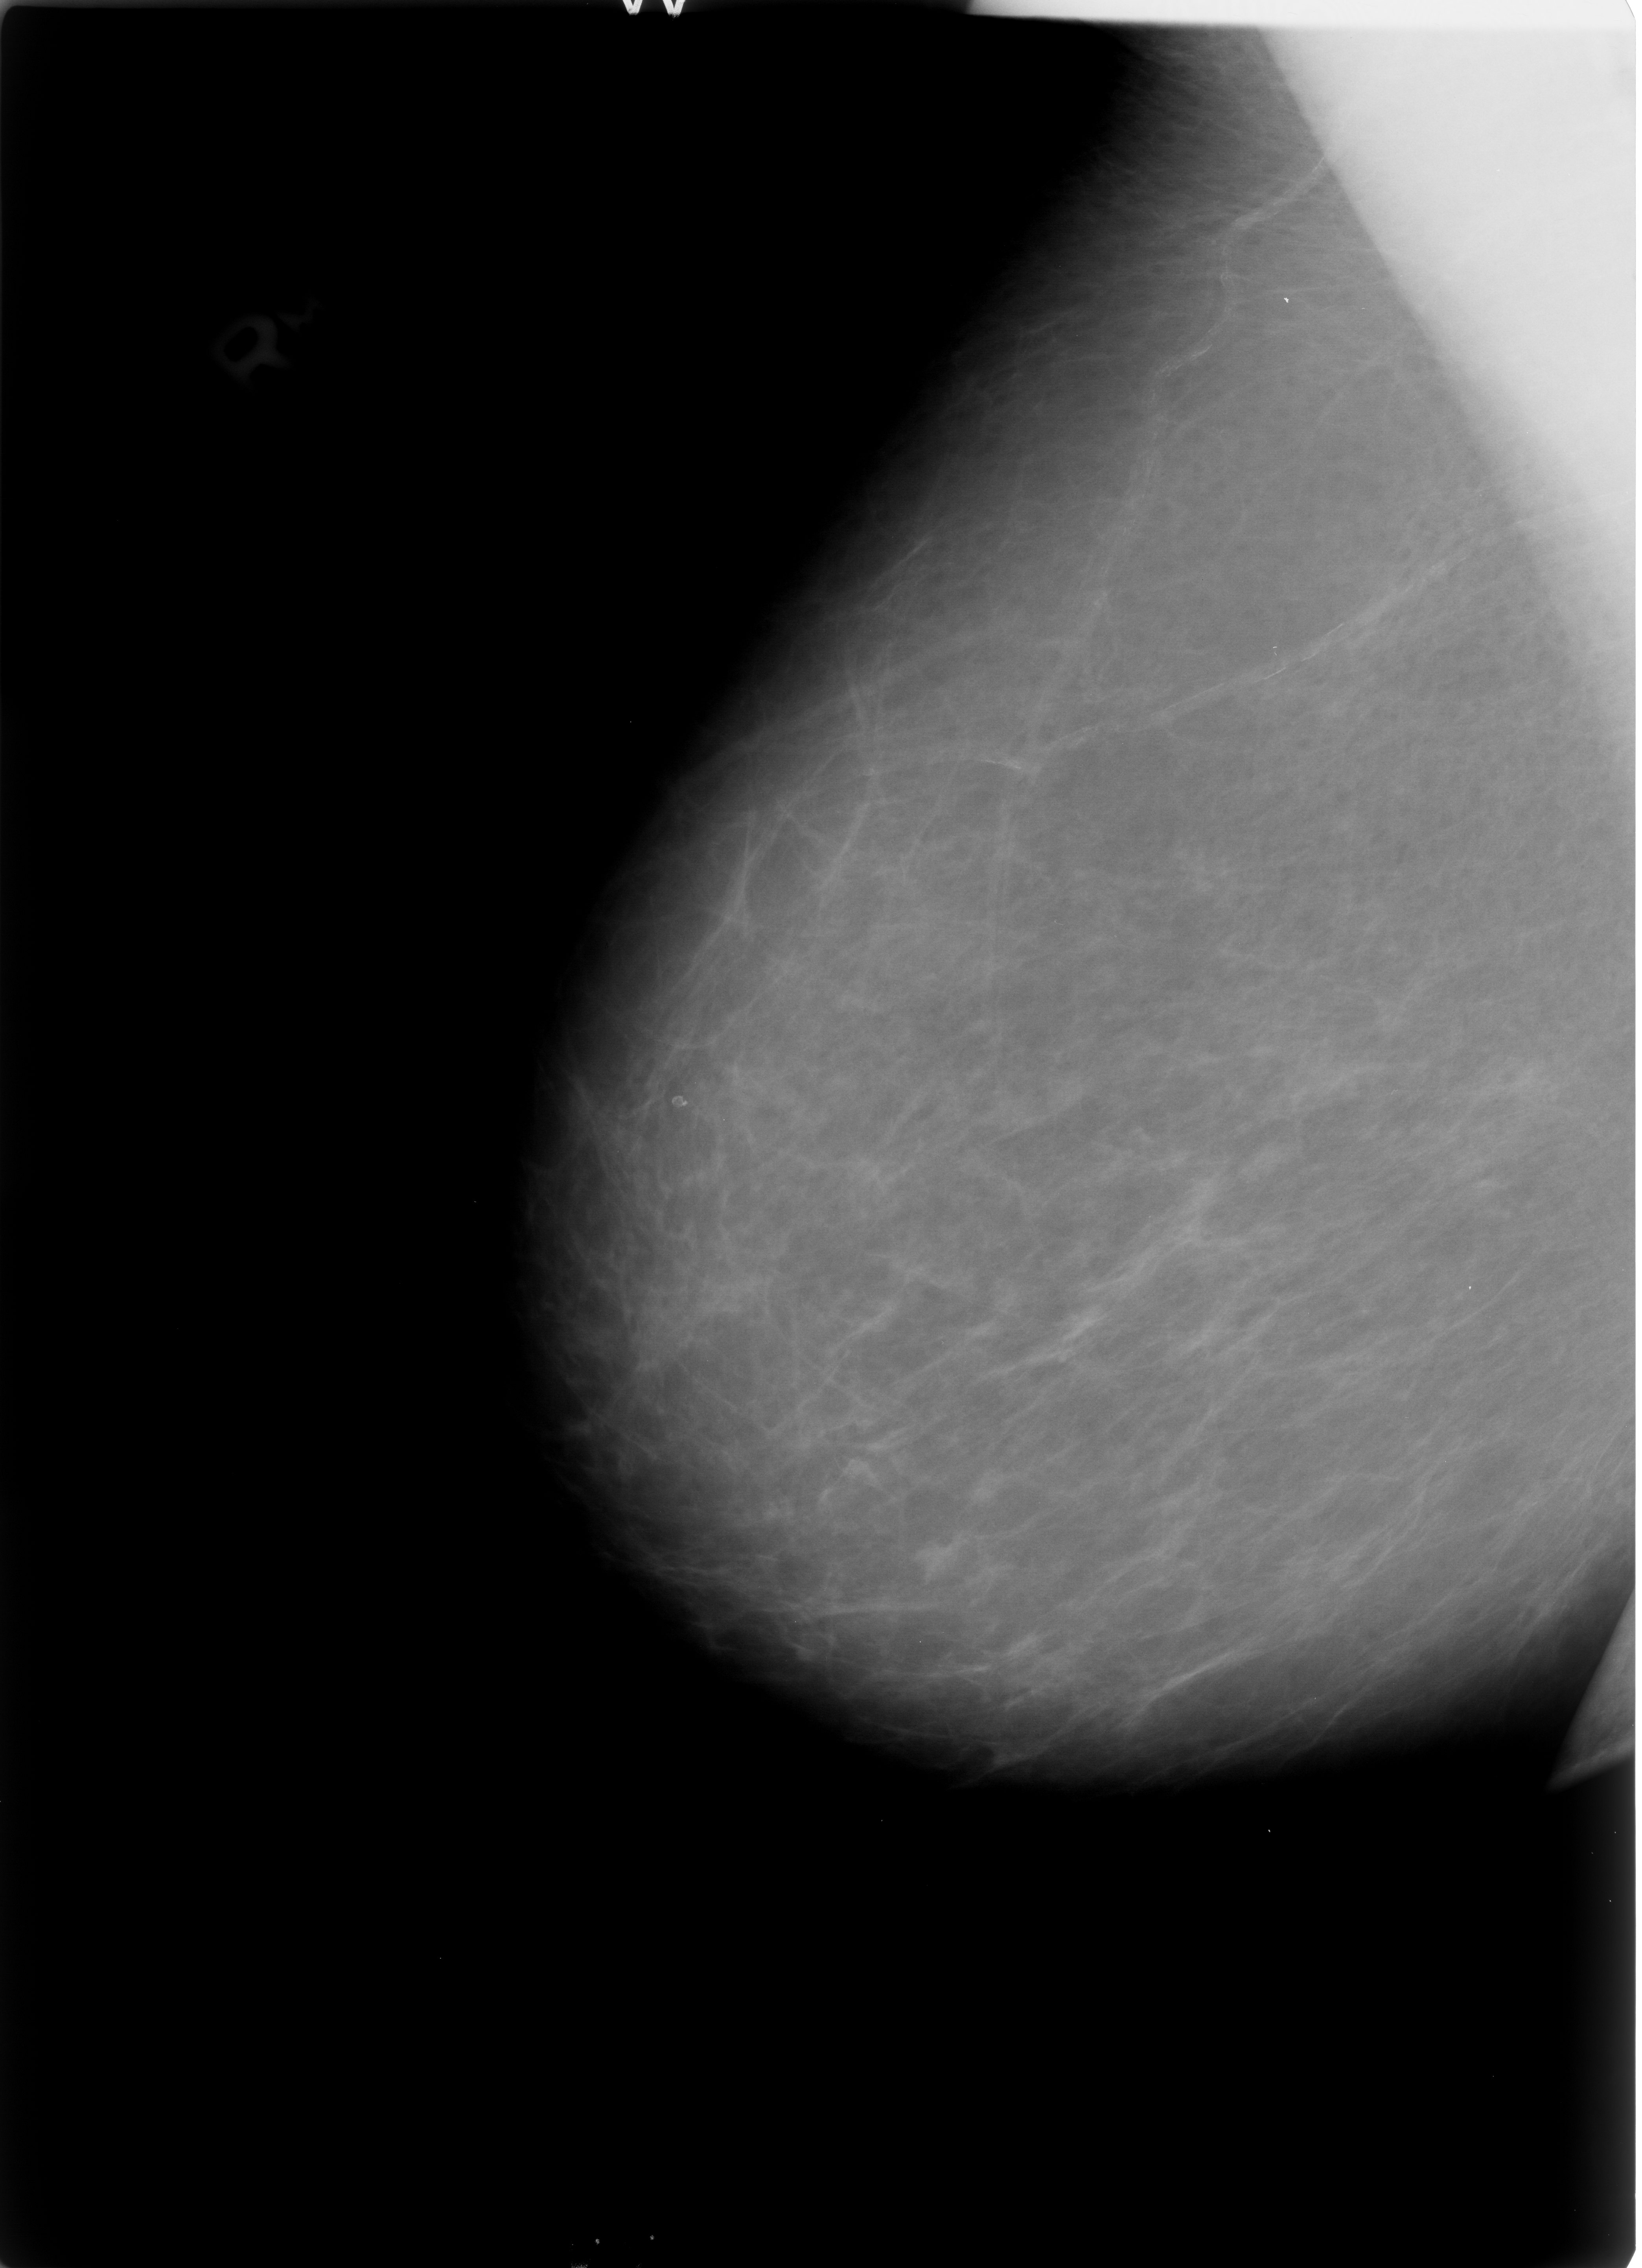
Mammogram (digitized film); right breast; MLO view; breast composition: almost entirely fatty (BI-RADS density category 1 of 4); 1642 × 2268 image matrix.
Marked abnormalities (boxes around the expert regions of interest):
- calcifications, morphology lucent centered; BI-RADS assessment category 2; subtlety rating 3 on a 1 (subtle) to 5 (obvious) scale; outcome (as recorded, no biopsy): benign without callback (not worked up further): bounding box <663,1085,693,1118> (left, top, right, bottom; pixels)